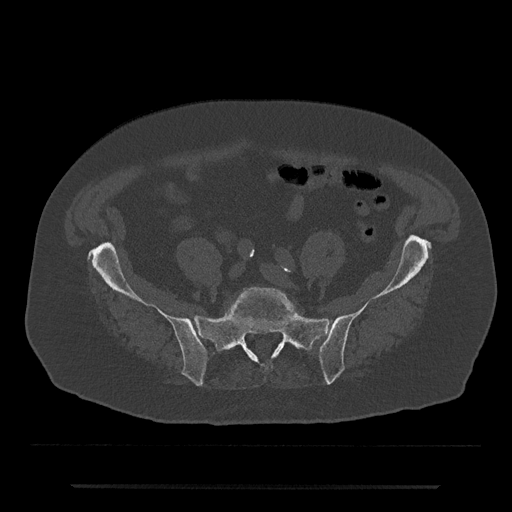
CT including the spine, one axial slice. Slice 249 of 797 in the series (ordered by position). Reconstruction kernel Br40s/3. Bone window (W 1800 / L 400 HU). 512 × 512 image matrix, field of view 434 × 434 mm. Male patient, age 80 years. Case-level facts recorded for this patient, not image findings: primary cancer: prostate.
Structures marked on this image (semi-automatically segmented with operator editing):
- L5 vertebra: bounding box [x1, y1, x2, y2] px = [227, 287, 299, 349]